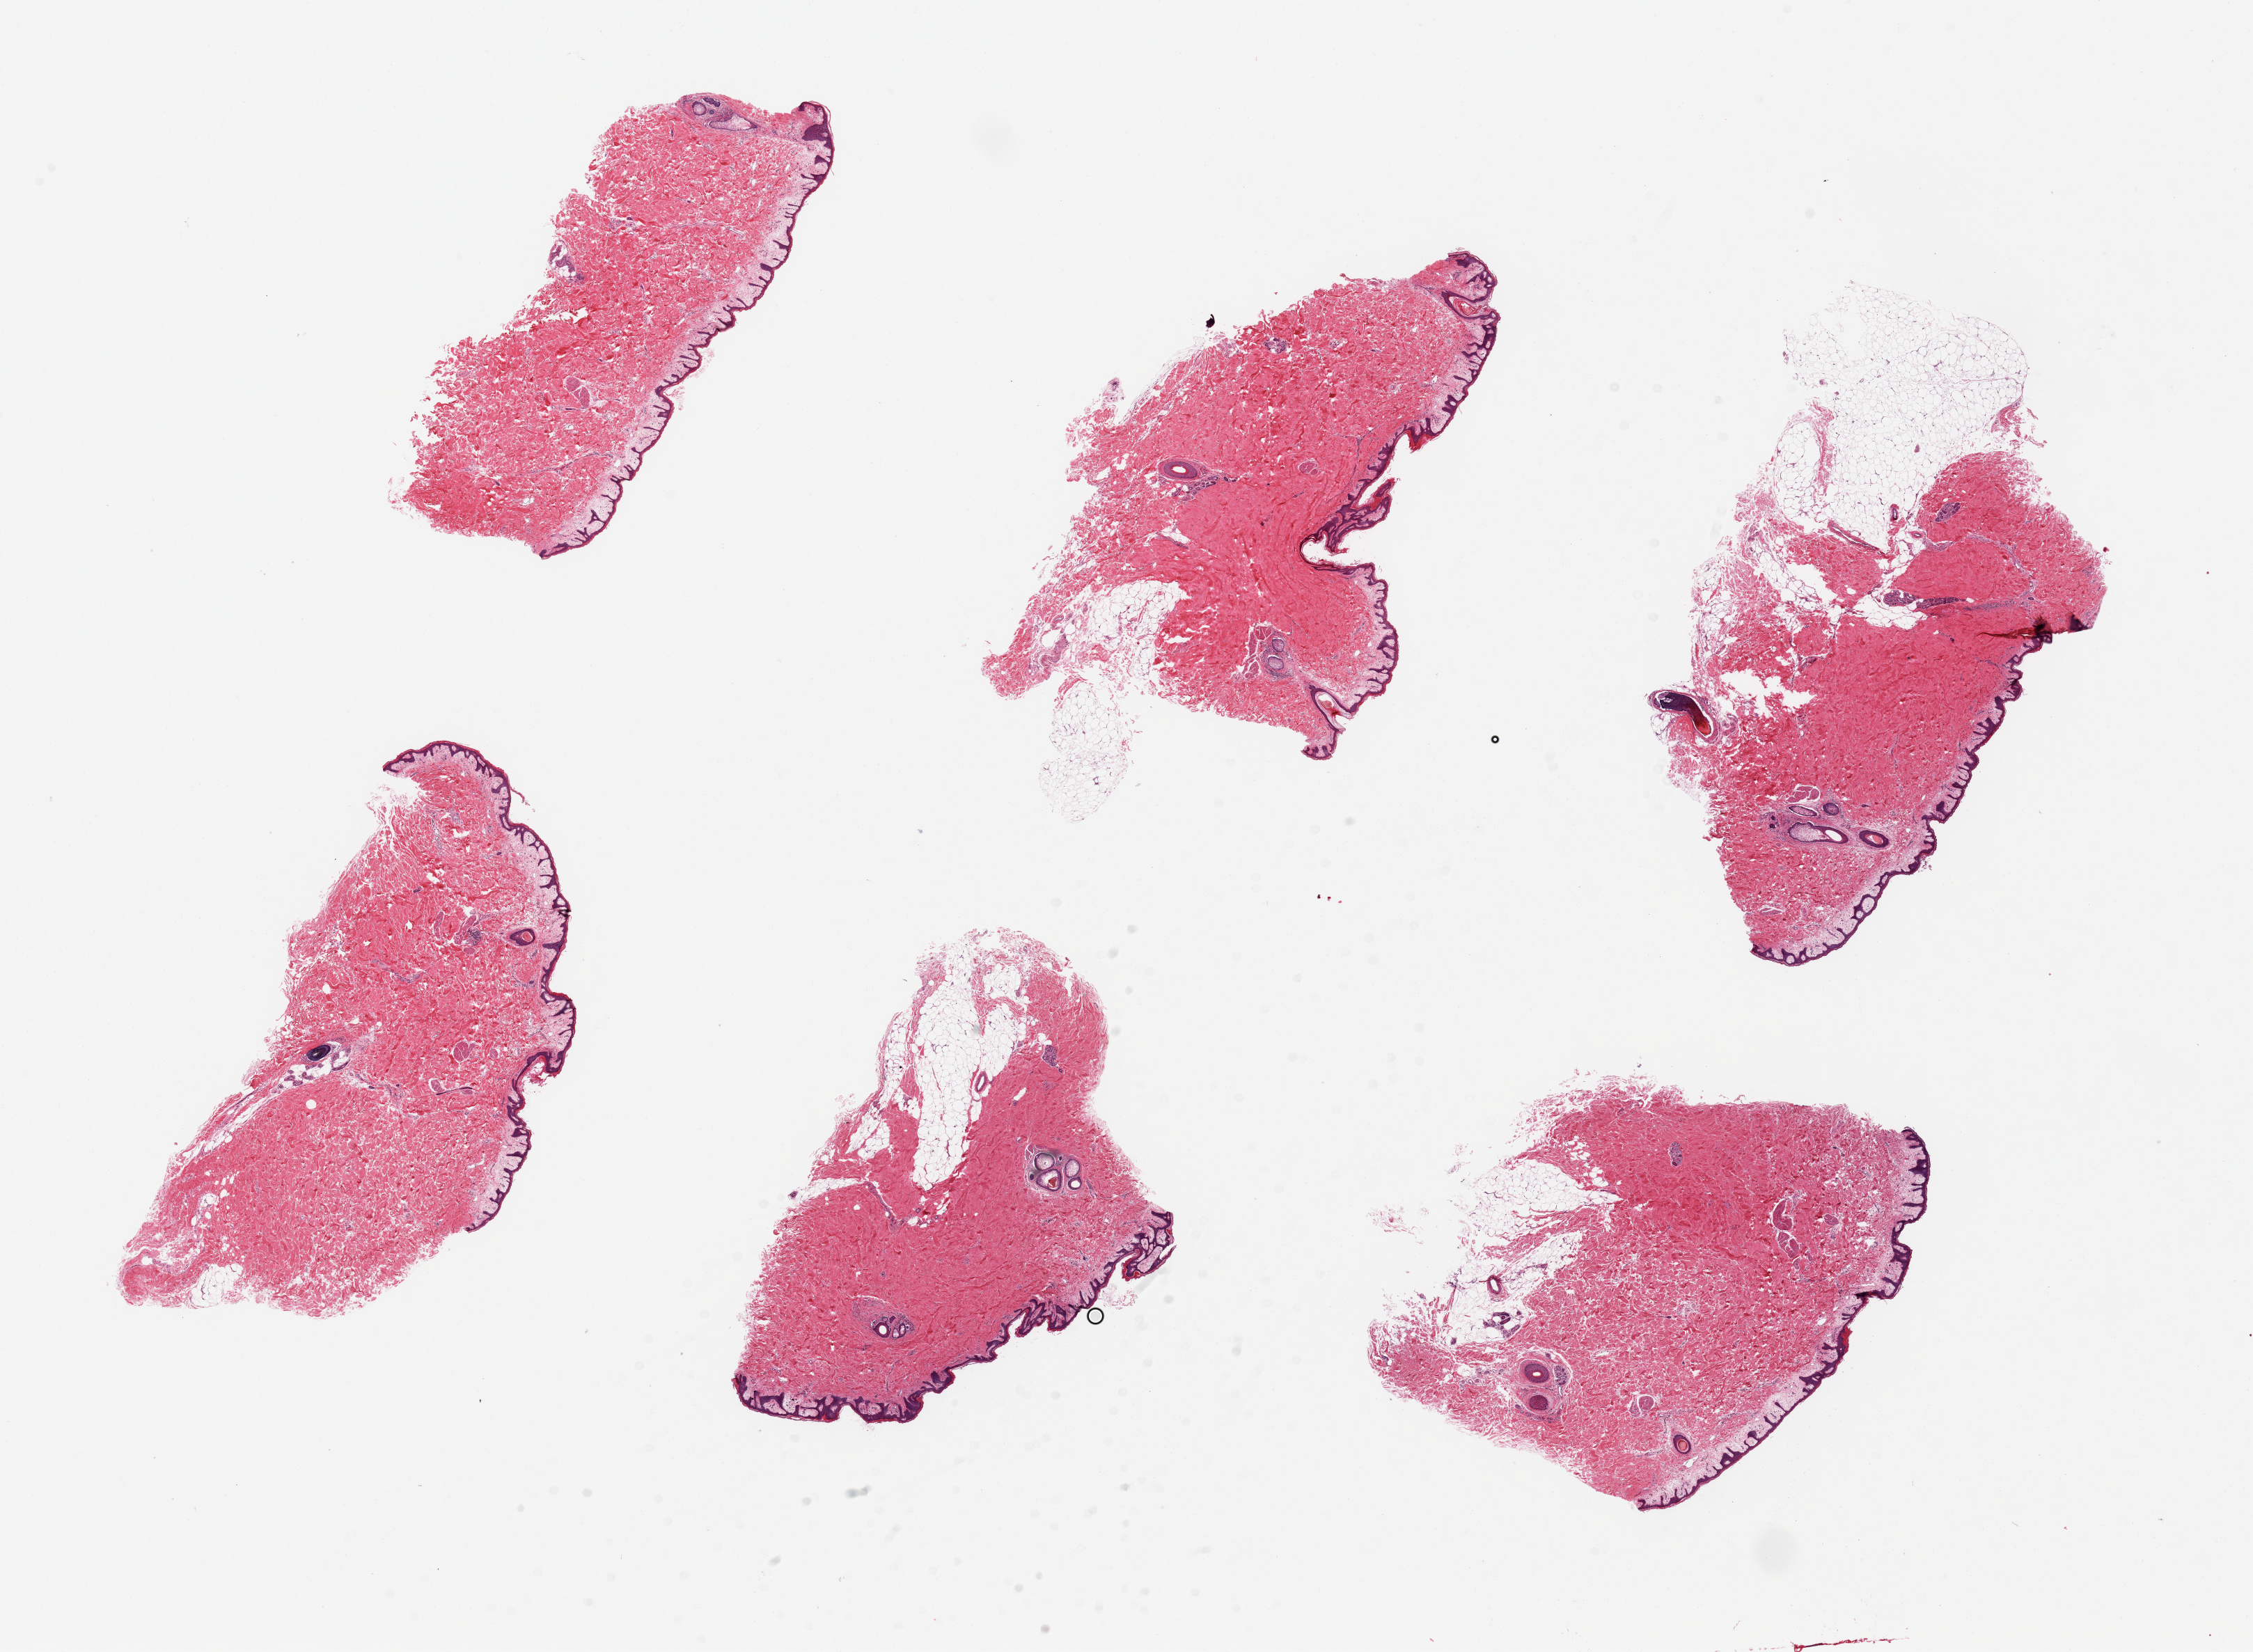
Haematoxylin and eosin whole-slide image, brightfield — whole scanned area (about 25.6 x 18.8 mm, slide scanned at 20x) shown as a low-resolution overview, PAXgene-fixed paraffin-embedded (PFPE) section, sampled site (target tissue): skin of suprapubic region, donor tissue sample. Donor sex: male.
Reviewer comment on this tissue sample: 6 pieces ~6x3mmatrophic squamous epithelium less than 1 % of thickness.